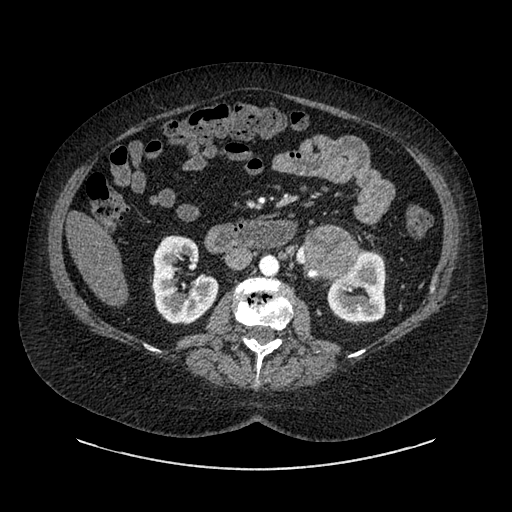
Contrast-enhanced abdominal CT, one axial slice; position 497 of 769 along the scan axis; reconstruction kernel SOFT; 120 kVp; soft-tissue window (W 400 / L 40 HU); 0.62 mm slice thickness; 512 × 512 image matrix, field of view 460 × 460 mm. Patient: female, 61 years. From the clinical record (not read from this slice): diagnosis: adrenocortical carcinoma; tumour side: left adrenal; tumour size at pathology: 13 cm; Ki-67 index: 79 %; stage (as recorded): 2.
Annotated regions visible in this slice (semi-automatically segmented with operator editing):
- mass: bounding box <309,231,356,276> (left, top, right, bottom; pixels)